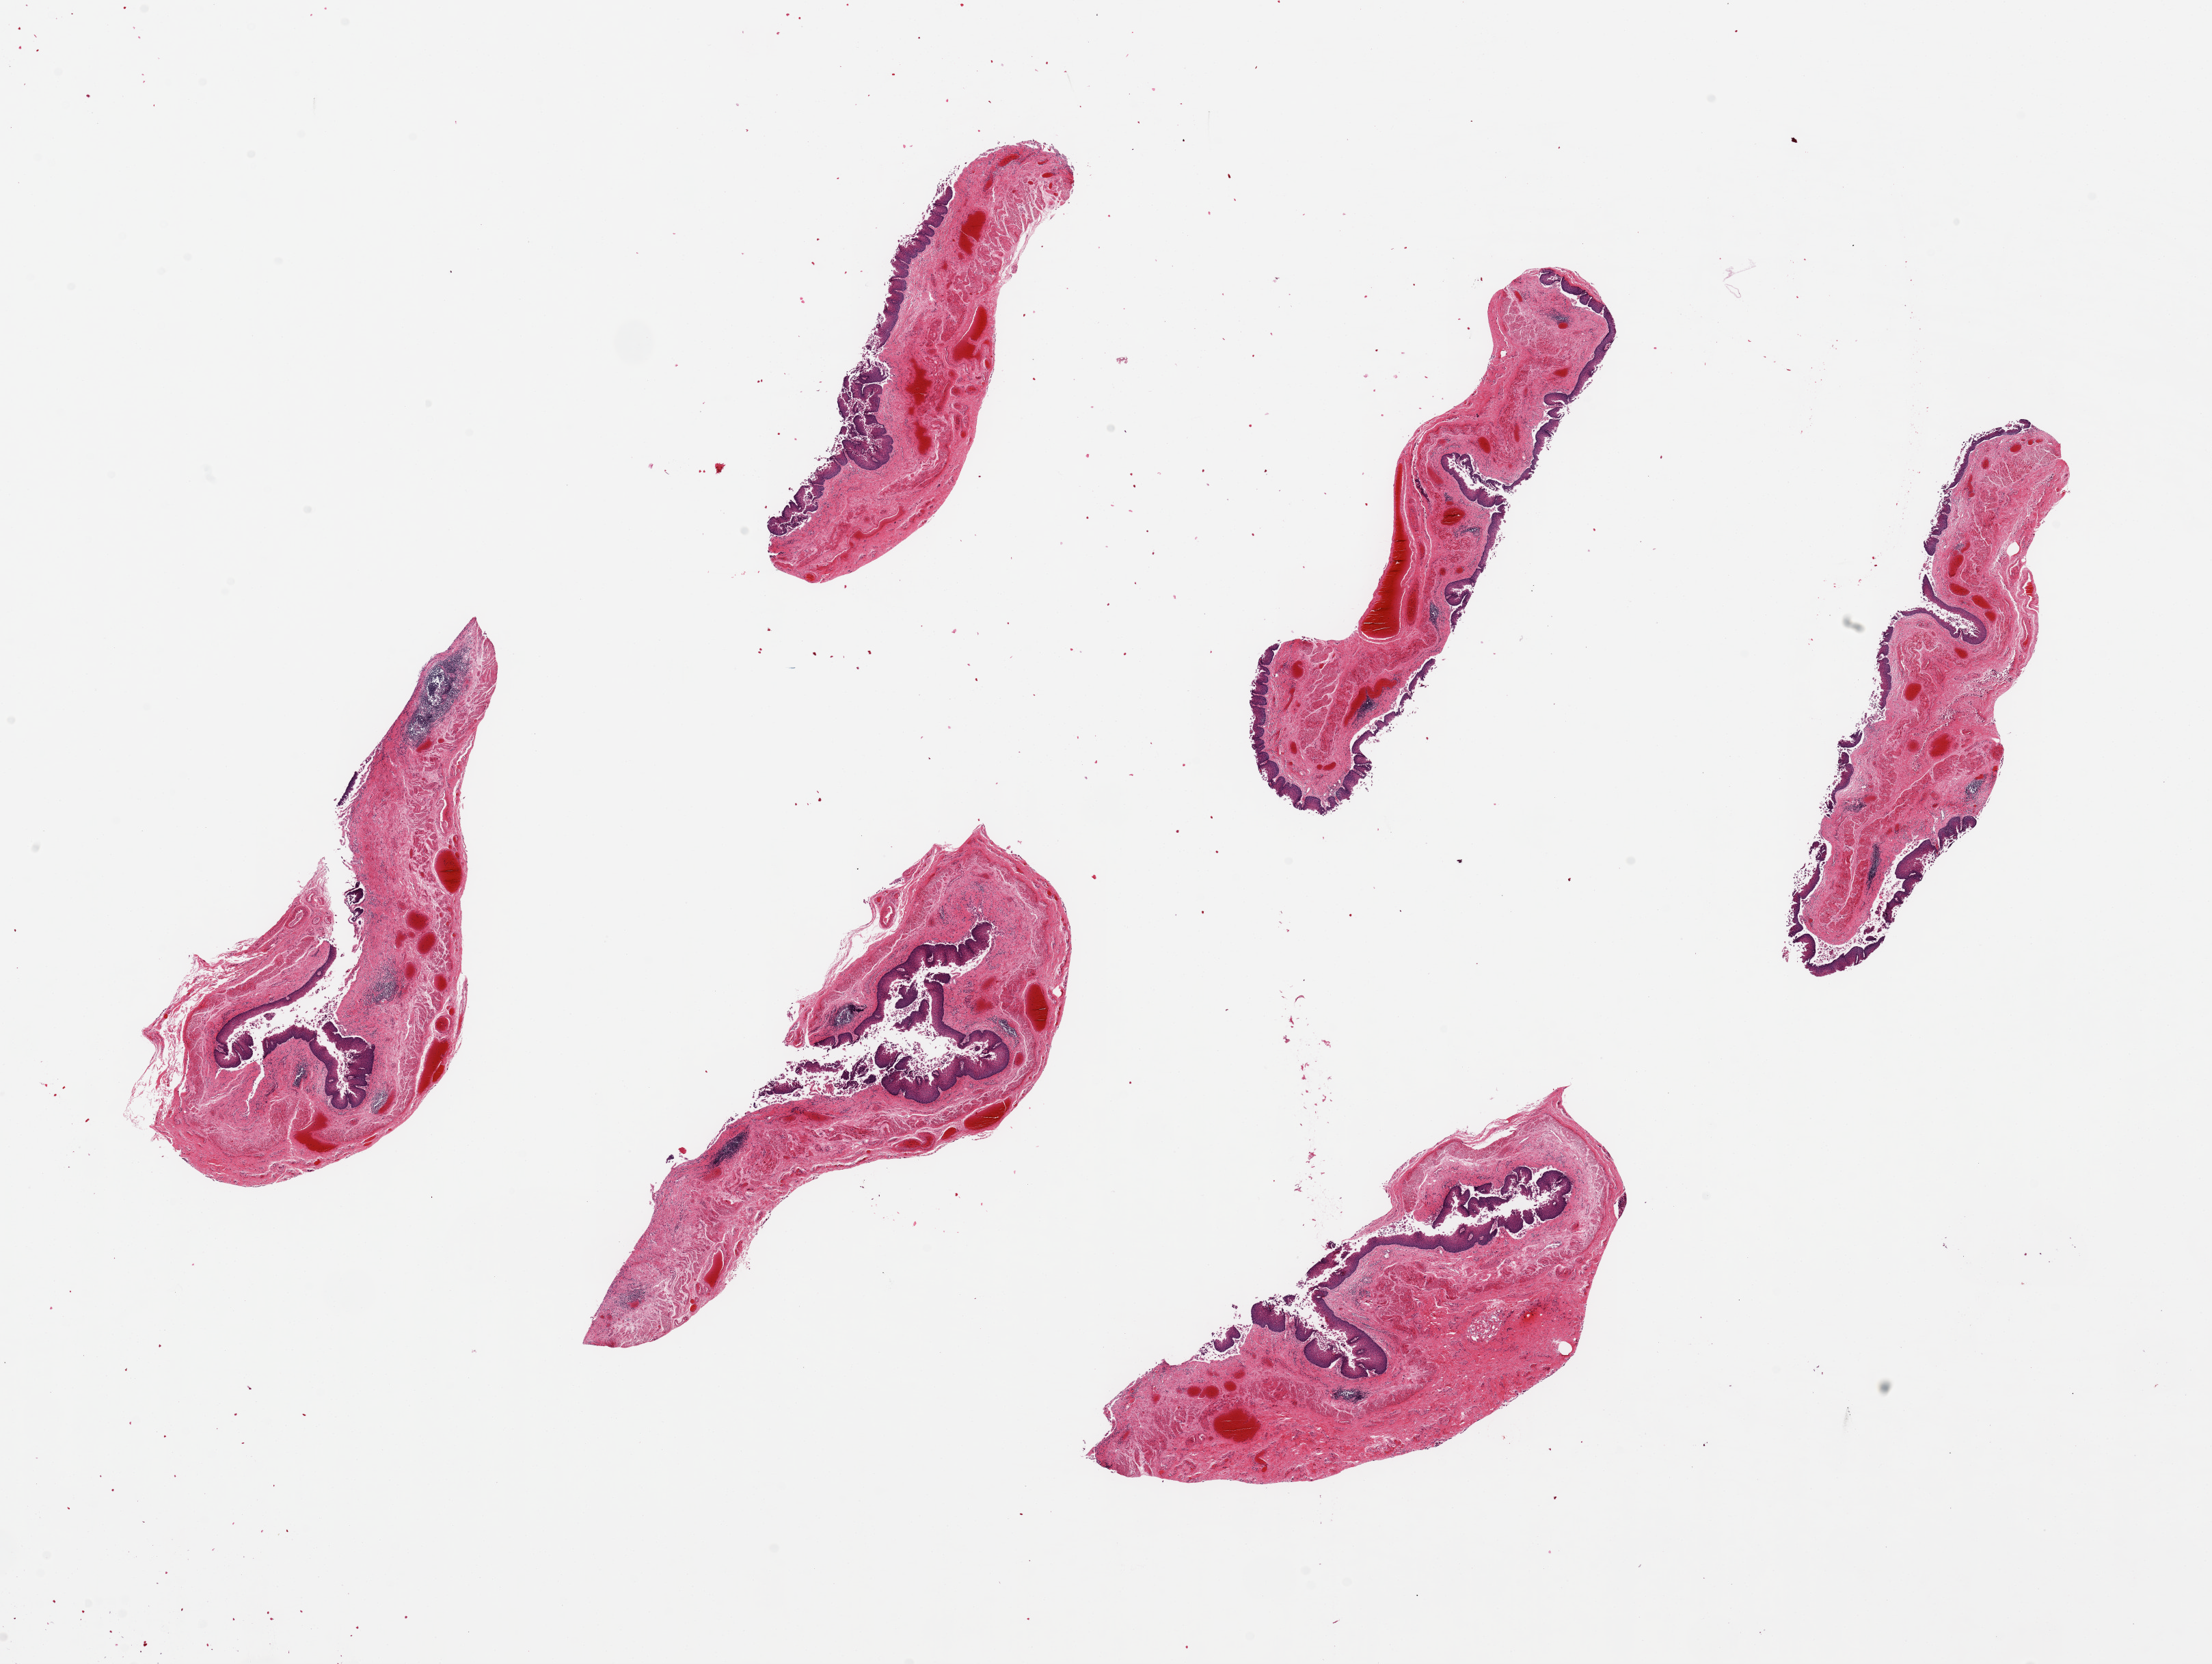
H&E whole-slide image — a low-resolution overview of the entire scanned area, about 25.6 x 19.3 mm. PAXgene-fixed, paraffin-embedded tissue. Target tissue: esophageal mucous membrane. Donor tissue sample. Male donor.
• pathologist's review note for this sample: 6 pieces ~6x1.5mm, squamous mucosa is badly autolyzed and sloughing